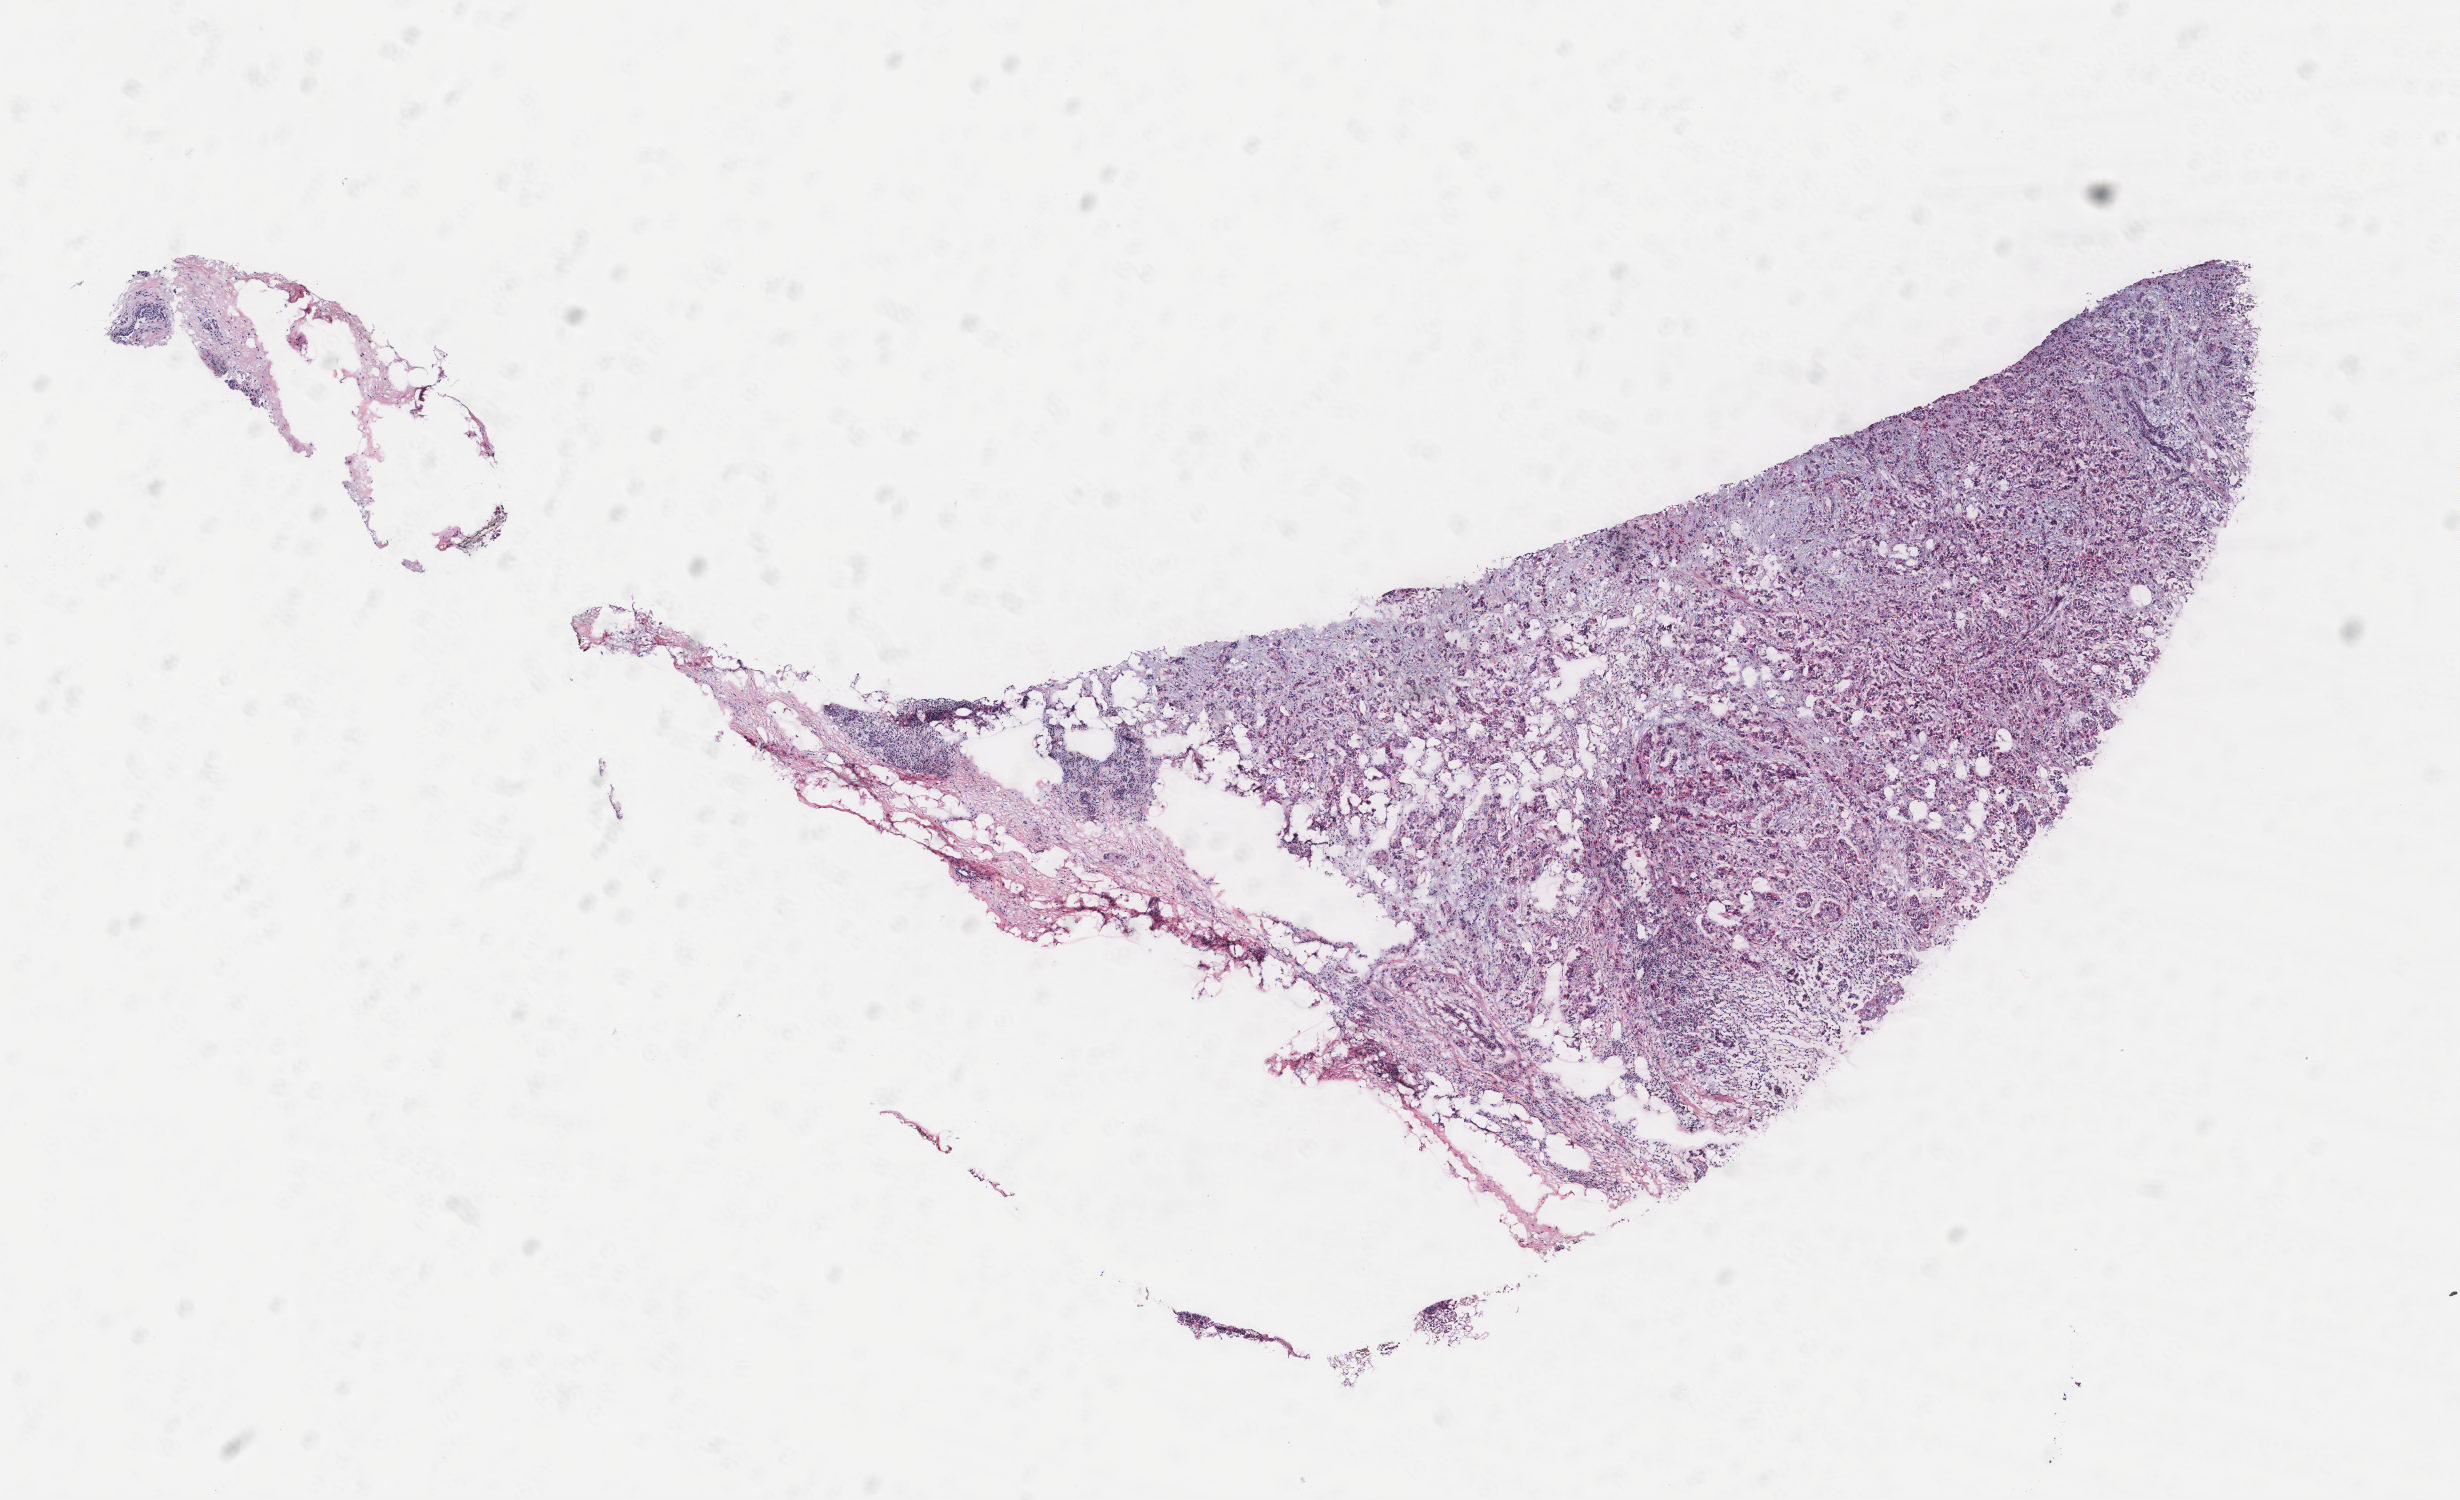
Whole-slide histology image, H&E — whole scanned area (about 9.8 x 6.0 mm, acquisition: 40x scan) shown as a low-resolution overview; breast, tissue type not recorded. 57-year-old female patient.
* patient diagnosis: Infiltrating duct carcinoma, NOS